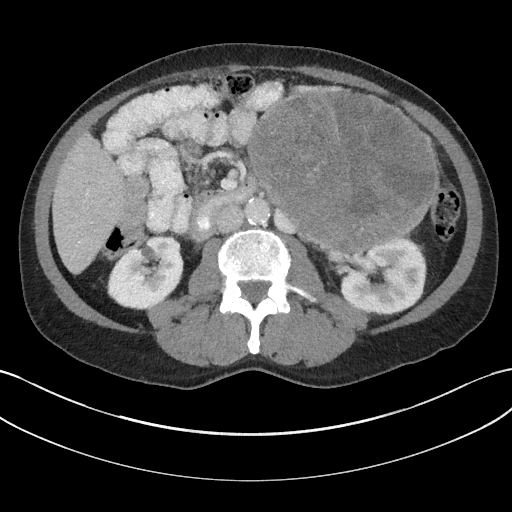
Contrast-enhanced abdominal CT, one axial slice; position 88 of 147 along the scan axis; 100 kVp; intravenous contrast given; soft-tissue window (W 400 / L 40 HU); 3 mm slice thickness; 512 × 512 image matrix. Patient: male, 58 years. From the clinical record (not read from this slice): diagnosis: adrenocortical carcinoma; tumour side: left adrenal; tumour size at pathology: 22 cm; Ki-67 index: 26 %; stage (as recorded): 2.
Outlined on this slice (semi-automatically segmented with operator editing):
- mass: bounding box <250,91,434,250> (left, top, right, bottom; pixels)